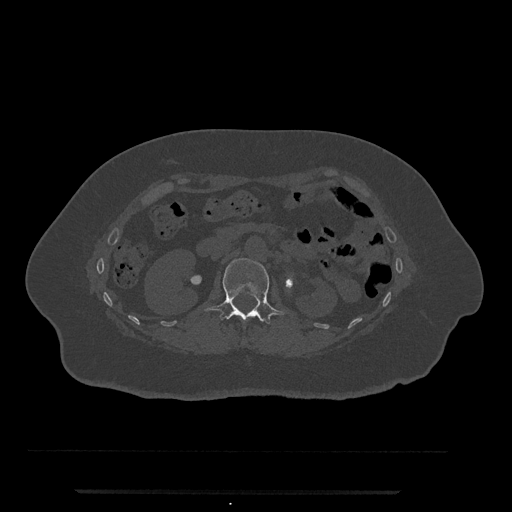
CT including the spine, one axial slice; position 105 of 797 along the scan axis; reconstruction kernel Br40s/3; bone window (W 1800 / L 400 HU); 0.5 mm slice thickness; 512 × 512 image matrix, field of view 440 × 440 mm. Patient: female, 51 years. From the clinical record (not read from this slice): primary cancer: neuro; vertebrae with lytic lesions (as recorded): T8.
Structures marked on this image (semi-automatic segmentation, software-assisted and operator-edited):
- L1 vertebra: bounding box (x1, y1, x2, y2) in pixels: (204, 258, 285, 324)